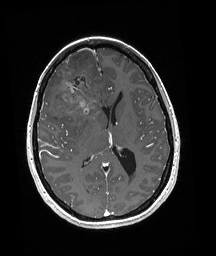
Brain MRI from a brain-tumour surgery series, one axial slice. Position 90 of 192 along the scan axis. T1-weighted post-contrast. 216 × 256 image matrix, field of view 211 × 250 mm. Case-level facts recorded for this patient, not image findings: histopathology: Oligodendroglioma; WHO grade: 3; IDH mutation: yes; tumour location: Right Frontal.
Annotated regions visible in this slice (expert manual segmentation):
- tumour: bounding box (x1, y1, x2, y2) in pixels: (51, 63, 102, 118)